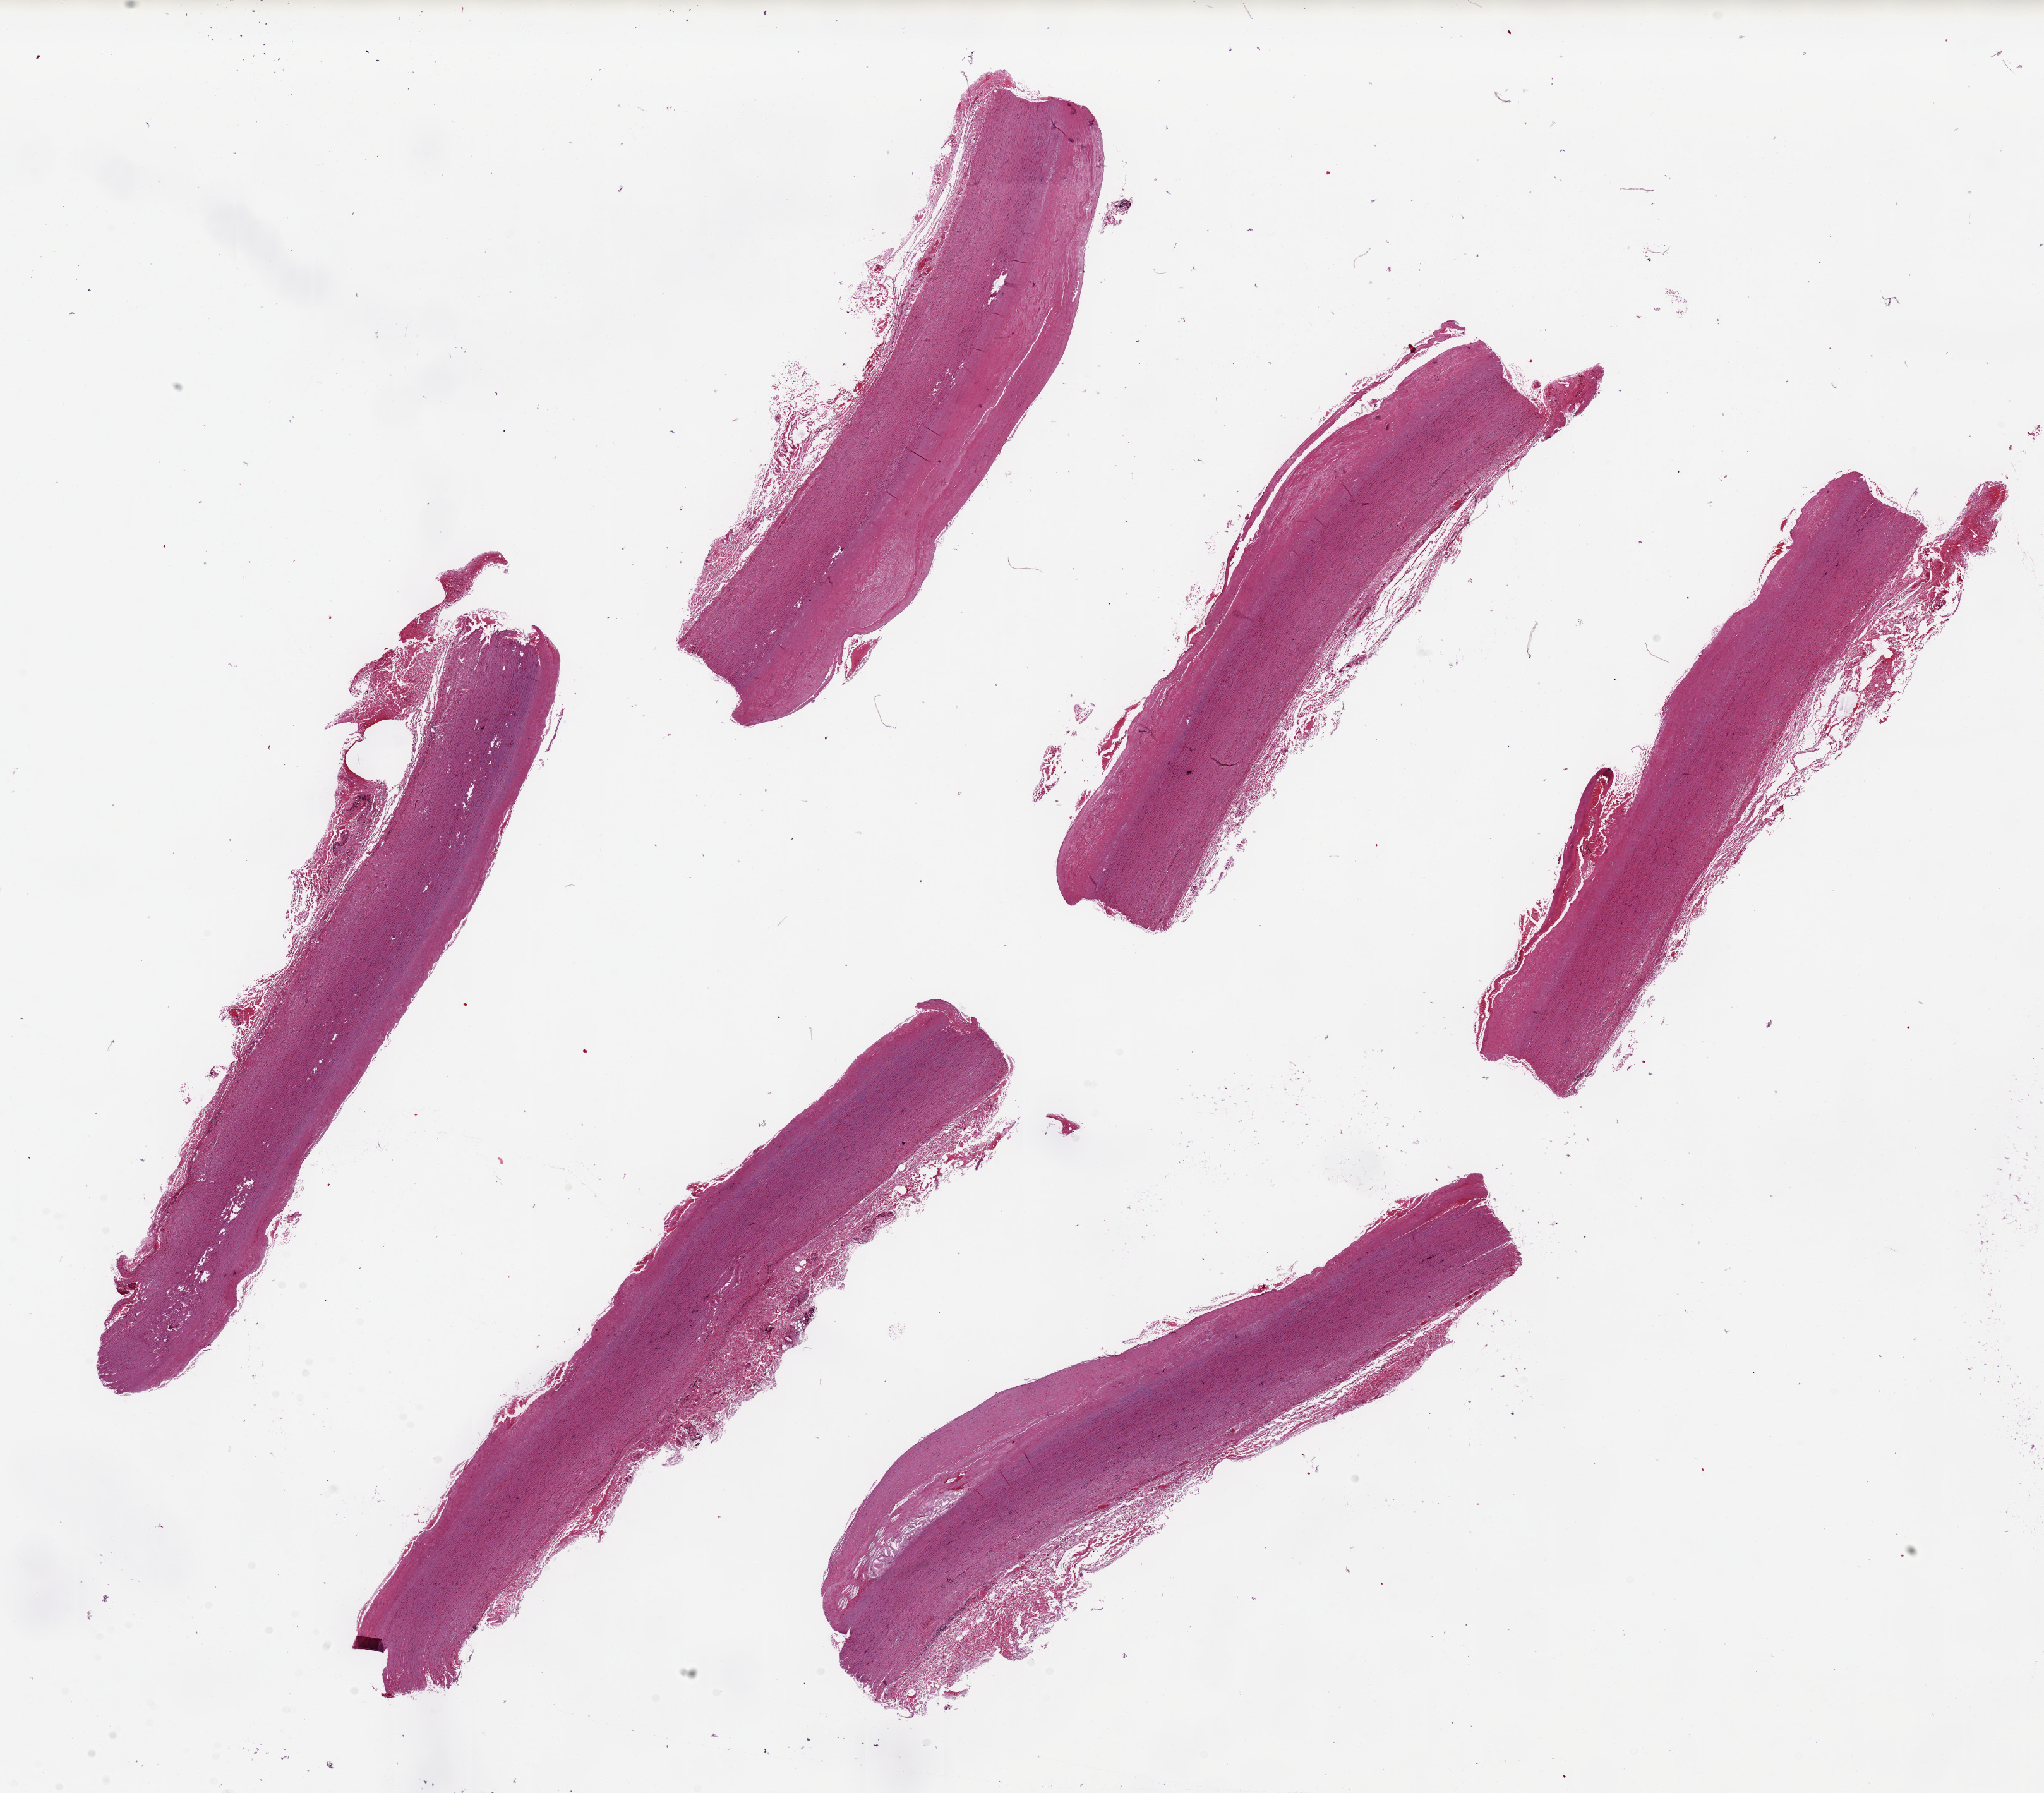
Digitized hematoxylin and eosin (H&E)-stained section, brightfield, a low-resolution overview of the entire scanned area, about 25.6 x 22.4 mm; PAXgene-fixed paraffin-embedded (PFPE) section; sampled site (target tissue): aorta; tissue donor sample. Donor sex: female.
* review note (as recorded): 6 ~9x1.5mm pieces, patchy atherosis